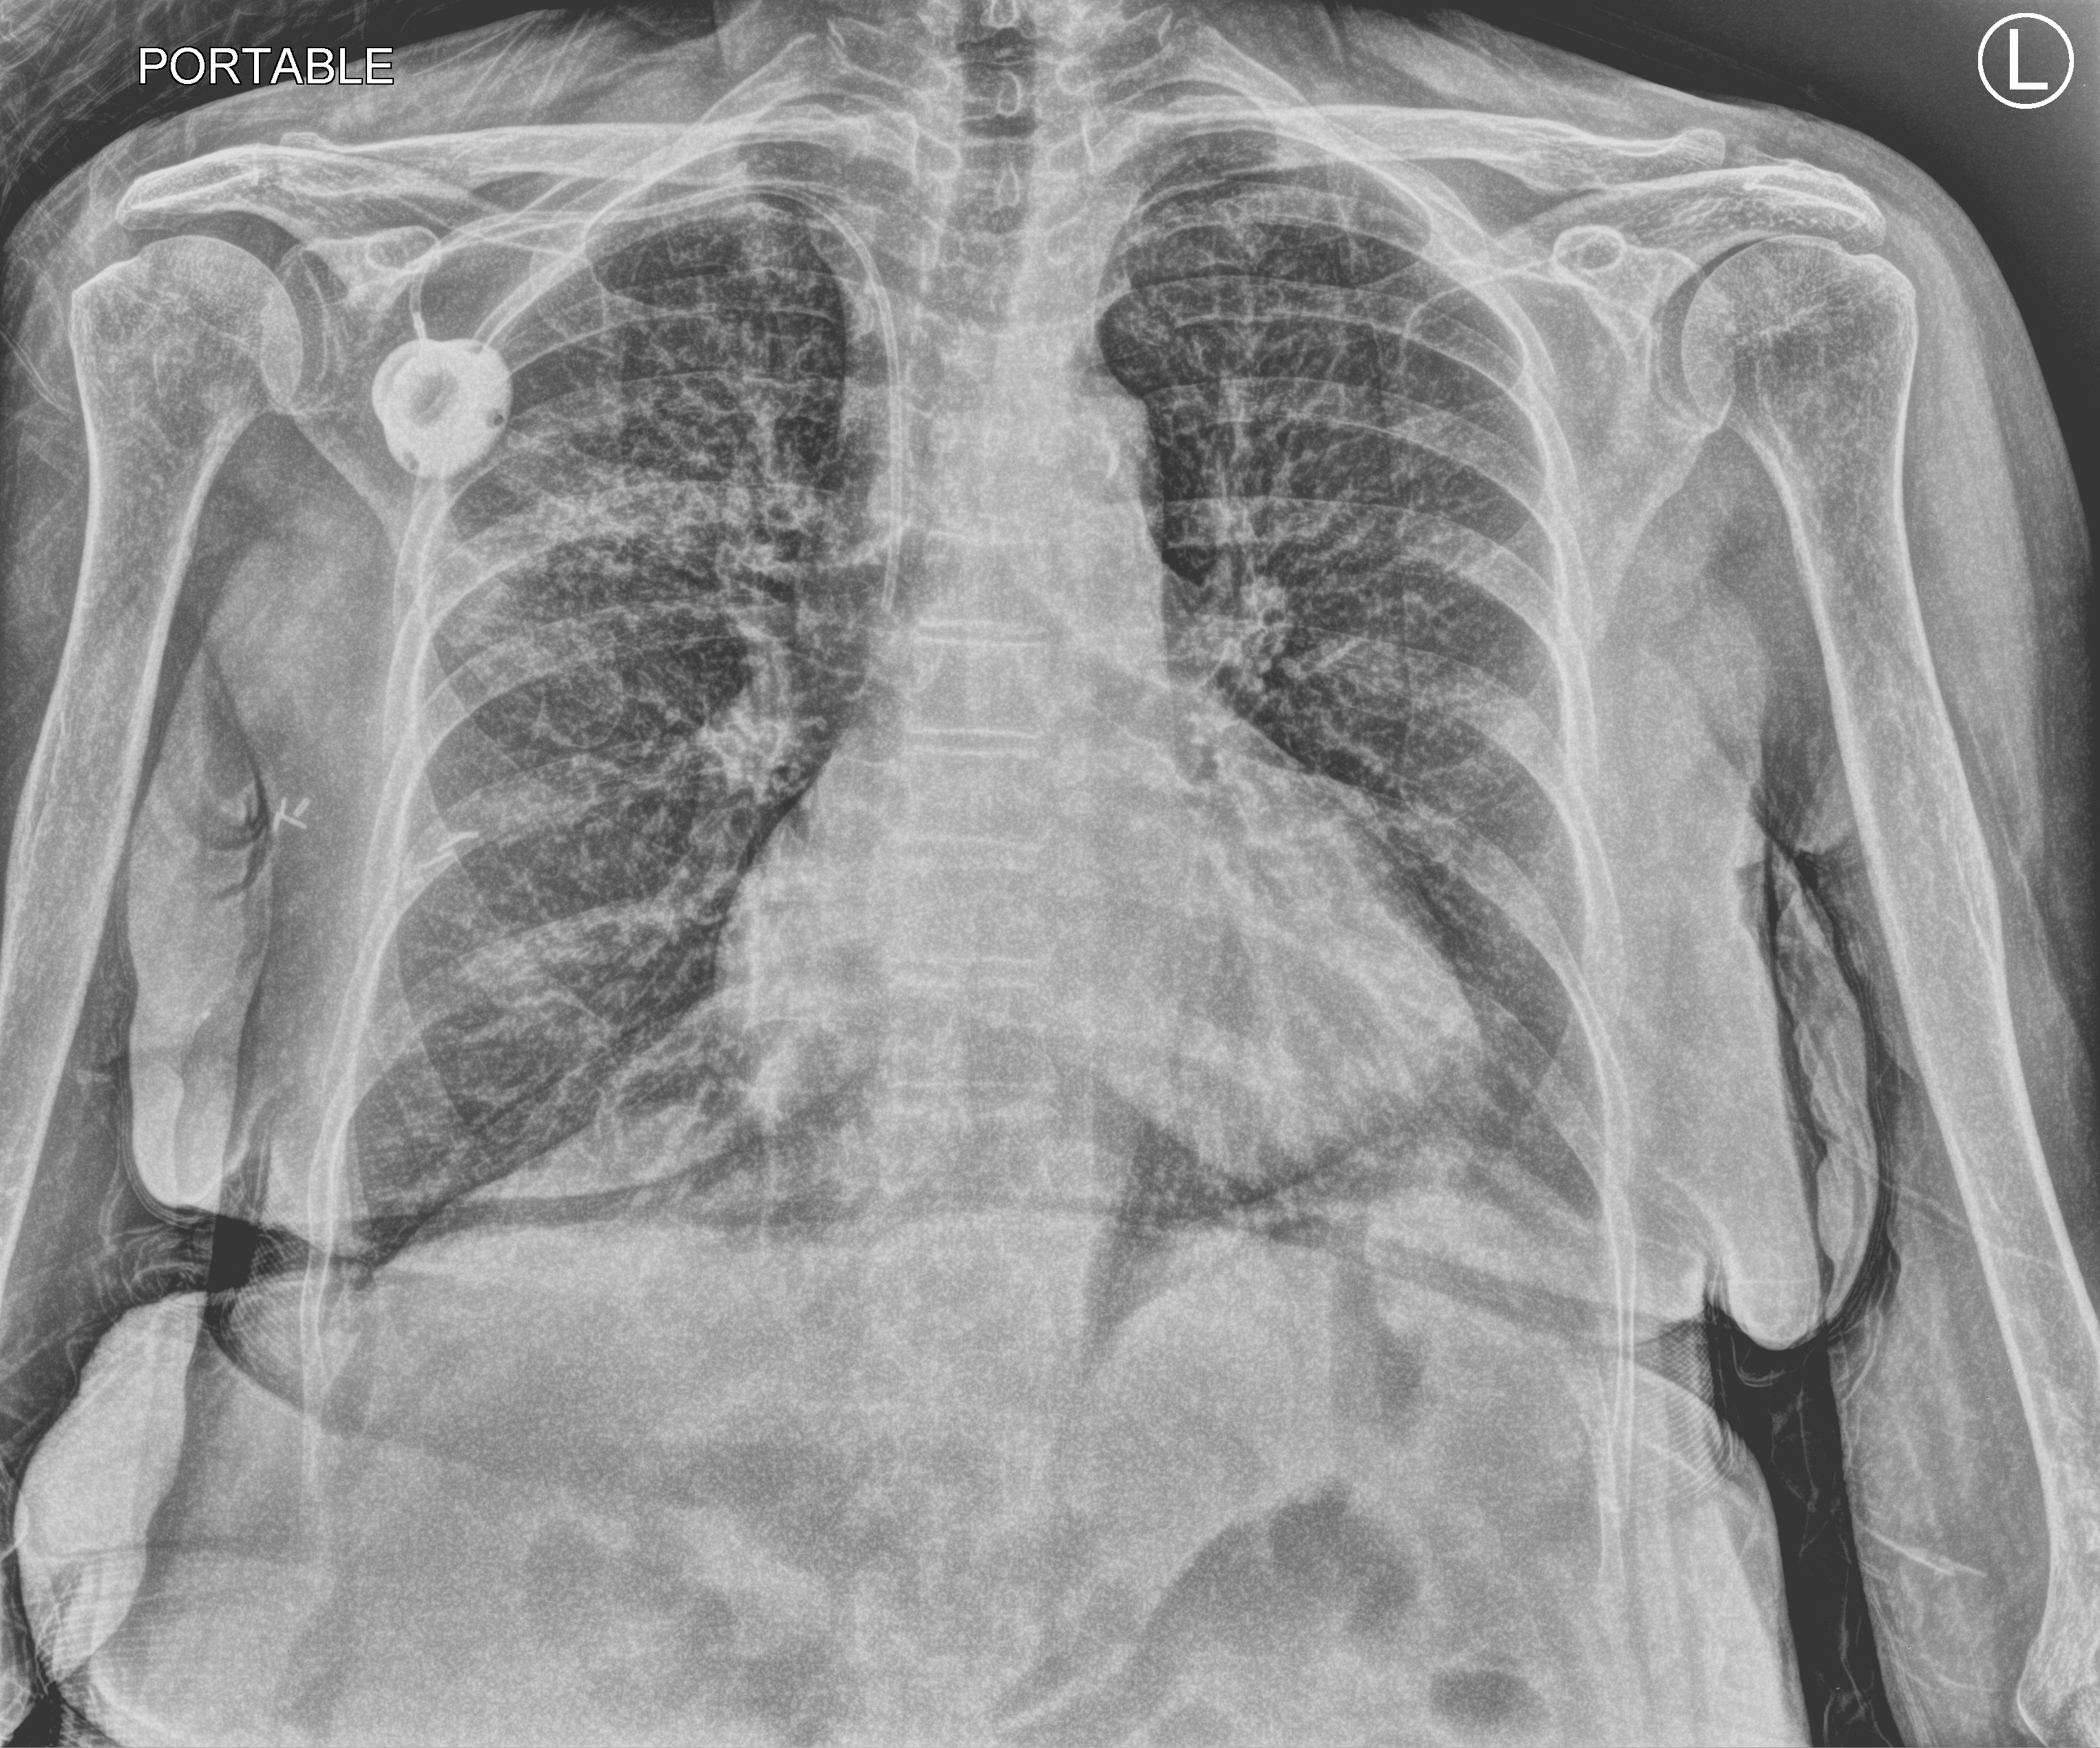
Chest X-ray (portable); anteroposterior (AP) projection. Patient hospitalised with COVID-19; female, aged 60–74 years.
Admission-level facts for this patient (not findings on this image; timing relative to this image not recorded): other chronic lung disease (admission record): no.